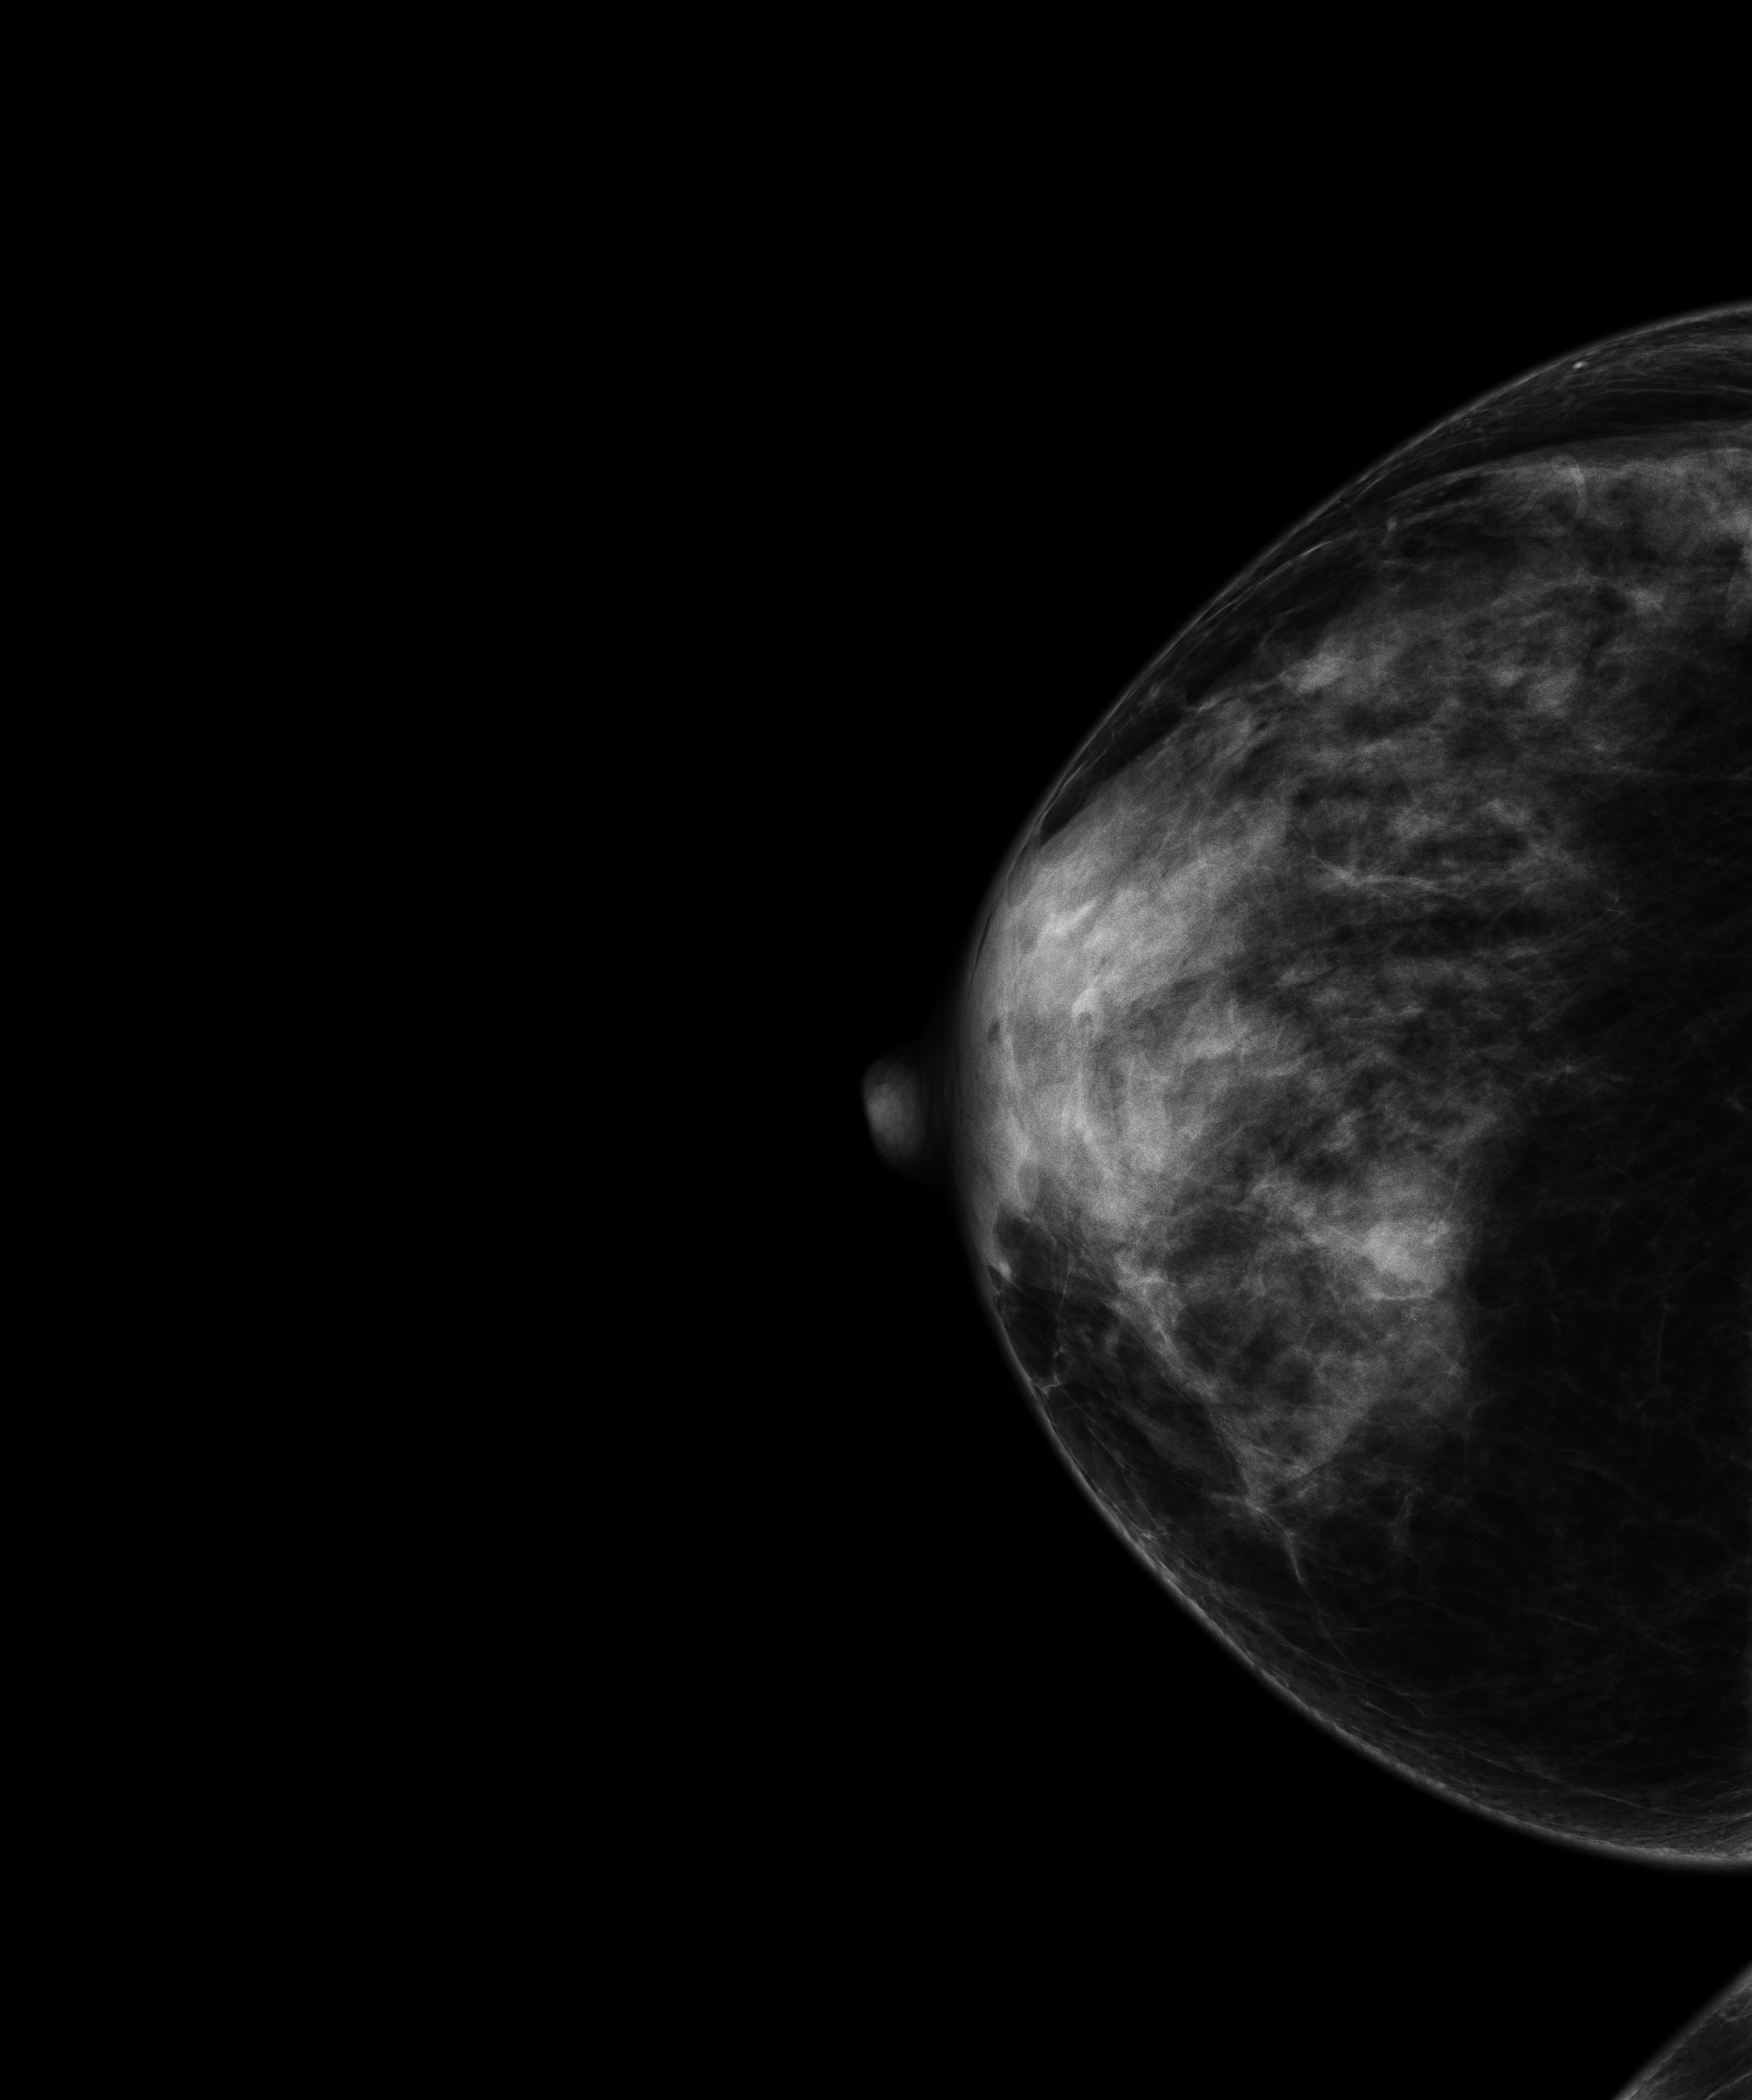
Full-field digital mammogram (FFDM); right breast; CC view; annual screening mammography examination; compressed breast thickness 37 mm. Patient aged 56 years (female).
Breast density at the screening exam (both breasts): extremely dense (BI-RADS density category d). Final BI-RADS category for the screening round (tomosynthesis exam, both breasts): category 1. Recall: no recall after this screen.